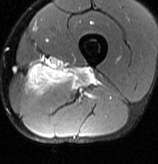
MRI of an extremity soft-tissue mass, one axial slice. Slice 22 of 70 in the series (ordered by position). T2-weighted fat-saturated. MR volume resampled by the dataset authors to the PET/CT grid (not the native acquisition matrix). 3.27 mm slice thickness. 158 × 164 image matrix. Male patient. From the clinical record (not read from this slice): histological type: extraskeletal osteosarcoma; grade: high; site of the primary tumour: left adductur.
Annotated regions visible in this slice (expert contour drawn on MRI and transferred to this co-registered scan by the dataset authors):
- gross tumour volume (mass): box from (x=24, y=64) to (x=98, y=93) px